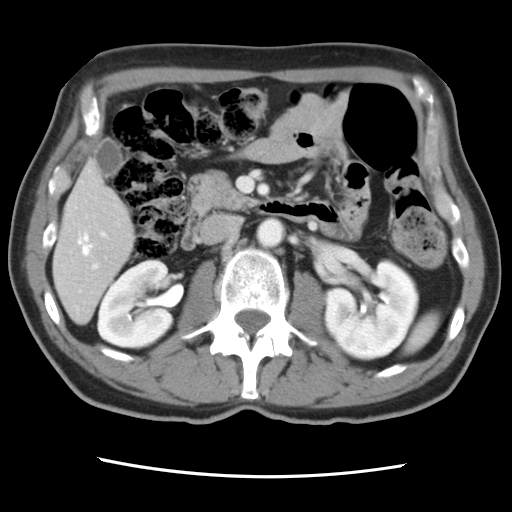
Contrast-enhanced abdominal CT, one axial slice; 120 kVp; intravenous contrast given; soft-tissue window (W 400 / L 40 HU); 5 mm slice thickness; 512 × 512 image matrix, field of view 321 × 321 mm. Male patient, age 69 years. Case-level facts recorded for this patient, not image findings: diagnosis: colorectal cancer liver metastases, imaged before liver resection; multiple liver metastases: yes; largest metastasis: 3.5 cm; disease in both lobes: no.
Structures marked on this image (outlined manually by an expert reader):
- hepatic veins: bounding box (x1, y1, x2, y2) in pixels: (78, 233, 92, 256)
- liver: (53, 164, 135, 322)
- planned liver remnant (the part of the liver to remain after resection): (53, 164, 136, 322)
- portal vein (with intrahepatic branches): (79, 231, 107, 293)